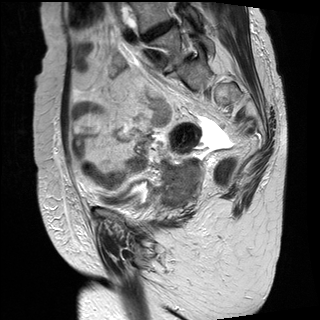
Pelvic MRI for cervical cancer, one sagittal slice; position 10 of 30 along the scan axis; T2-weighted; 1.5 T; TE 89 ms, TR 2930 ms; 320 × 320 image matrix, field of view 260 × 260 mm. Female patient, age 61 years.
Annotated regions visible in this slice (manually delineated by an expert):
- uterus and cervix: box from (x=159, y=157) to (x=206, y=208) px